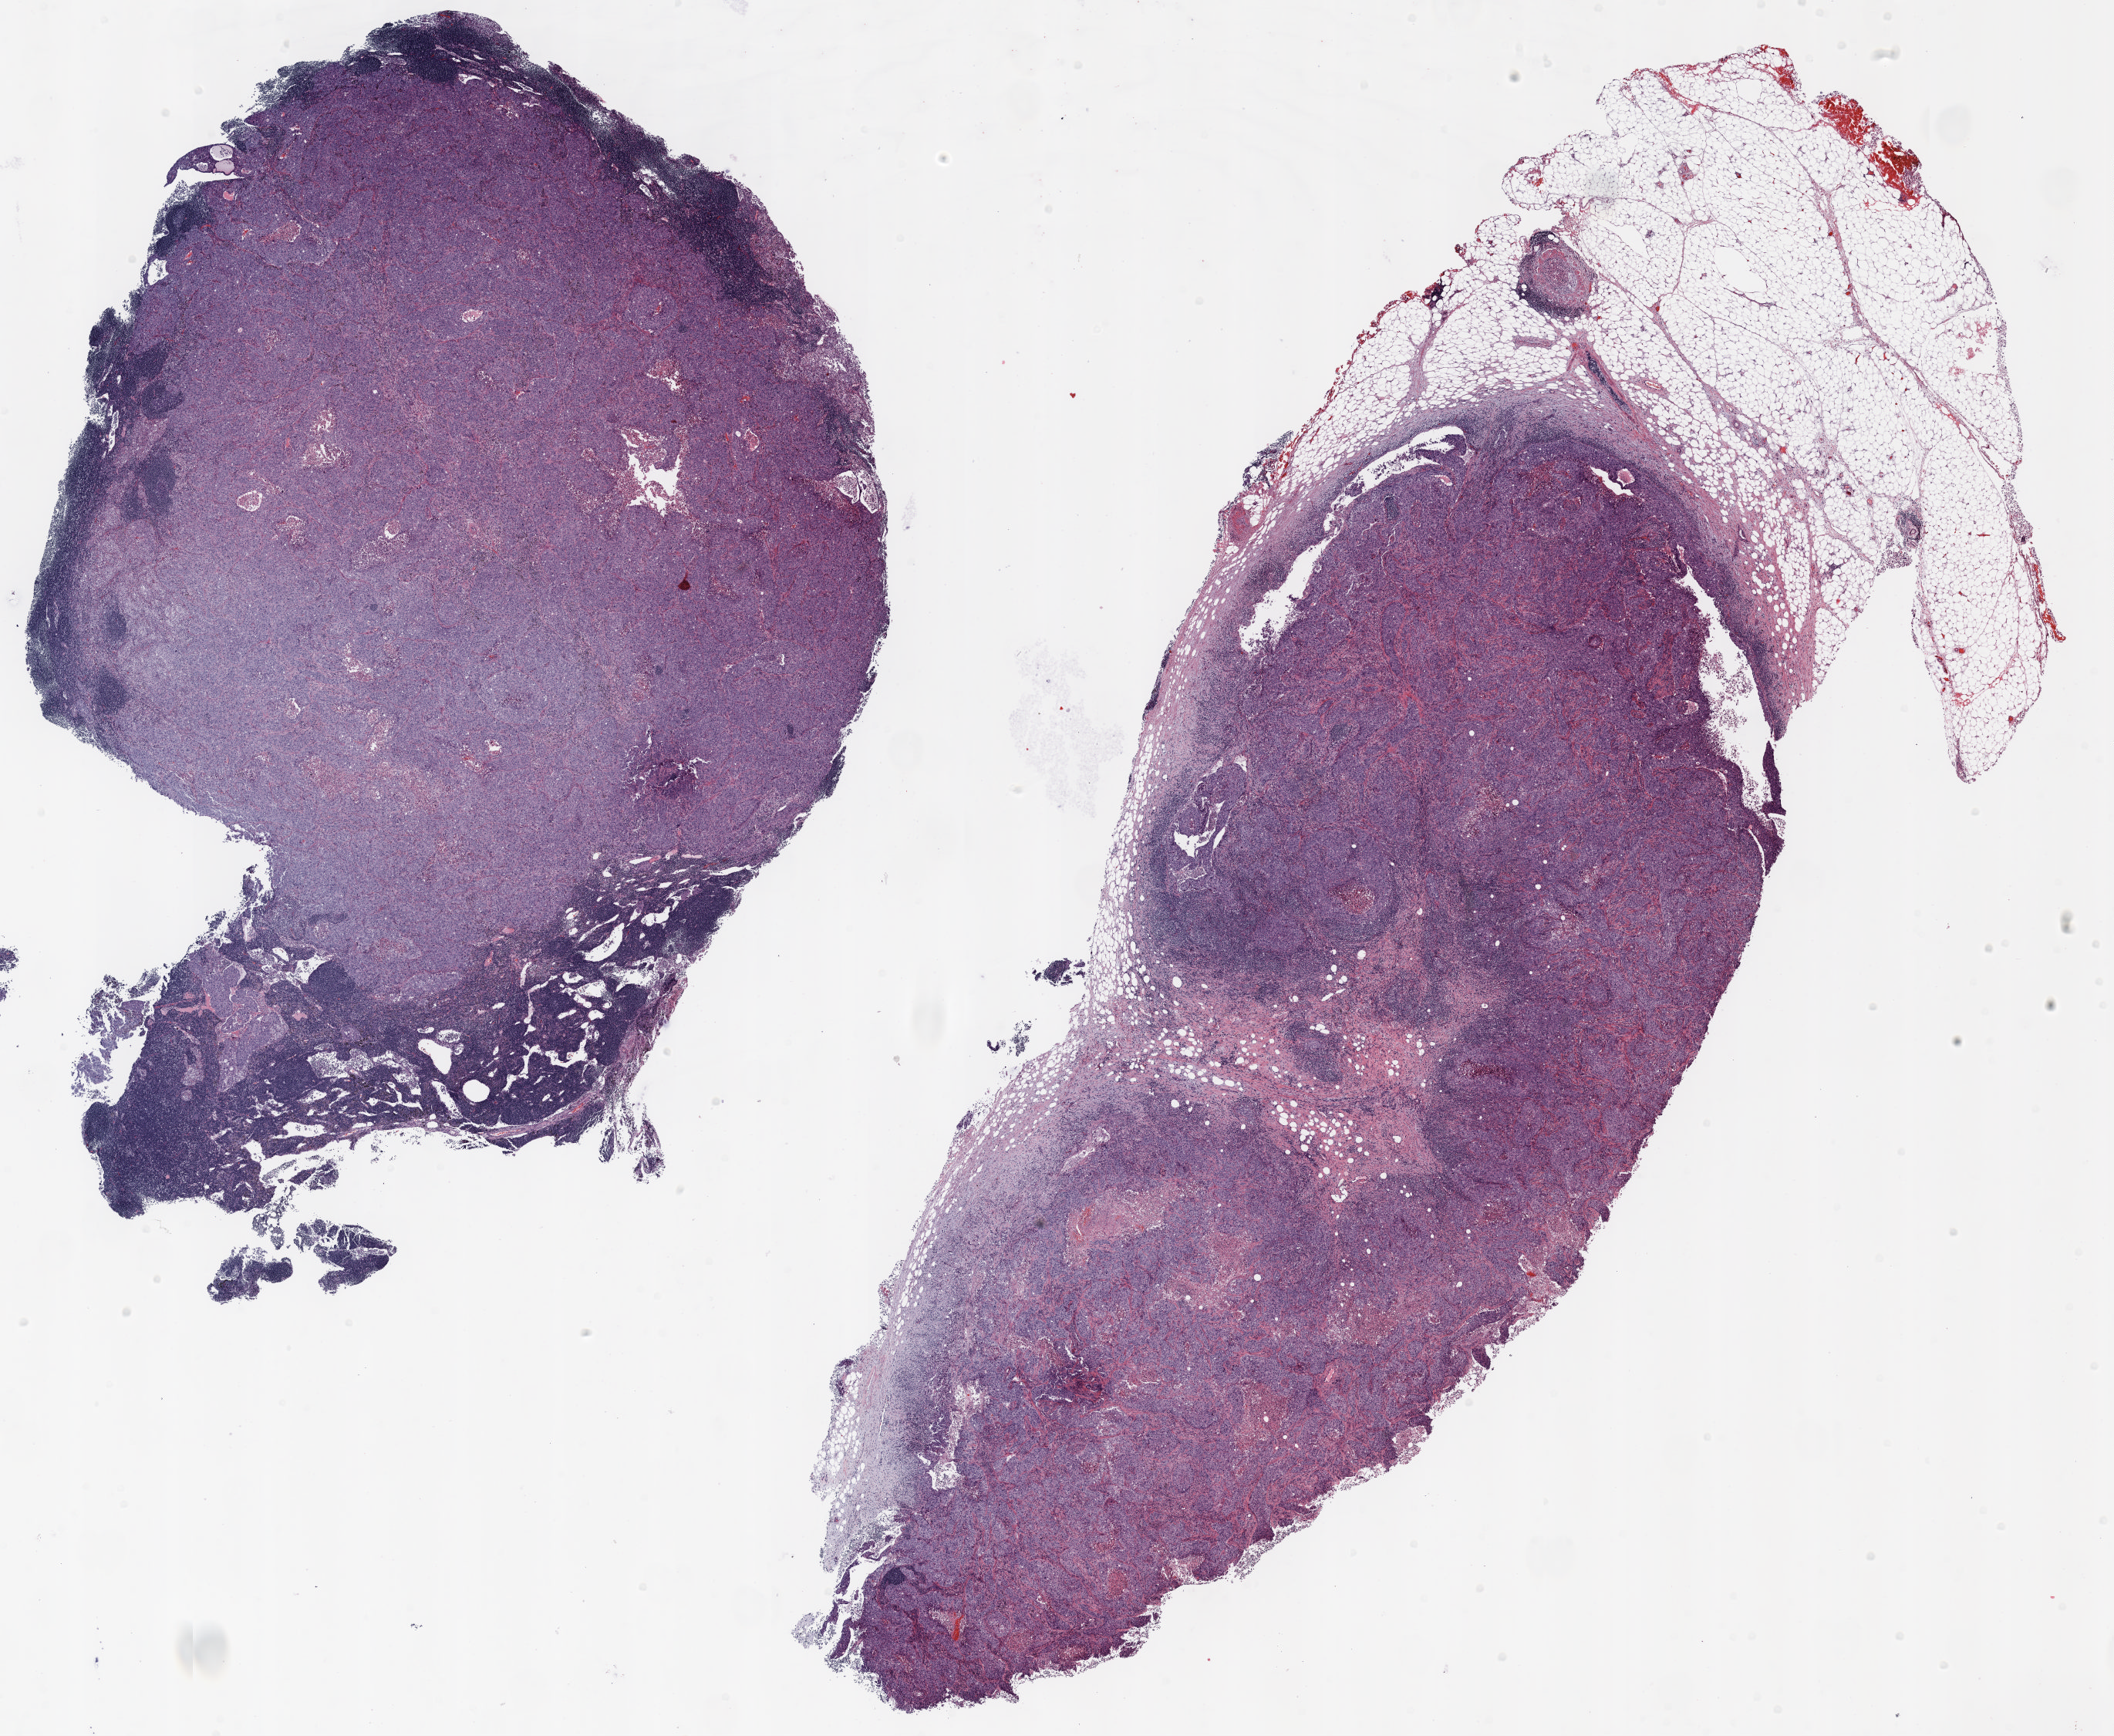
H&E-stained whole-slide image, low-resolution overview of the scanned area, about 22.0 x 18.1 mm (from a 20x scan), formalin-fixed paraffin-embedded (FFPE) section, lung. Male, age 61 at enrolment. Current smoker at enrolment. Grade: poorly differentiated (G3).
- tumour size (pathology): 30 mm
- stage (AJCC 6th edition): IIIA
- primary tumour location (clinical record): left upper lobe
- participant's lung-cancer diagnosis: Adenocarcinoma, NOS
- ICD-O-3 topography: upper lobe of lung (C34.1)